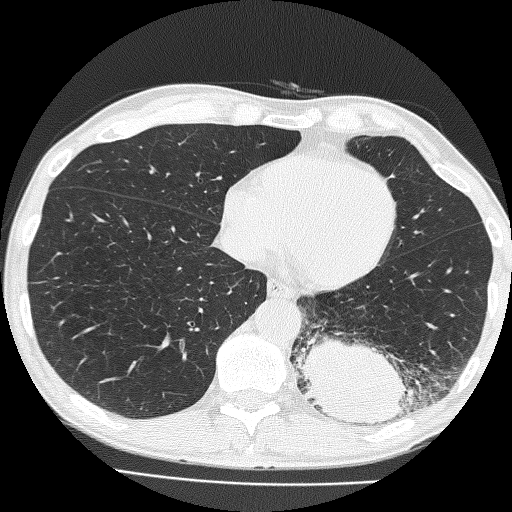
Low-dose screening chest CT, axial slice. Baseline annual screen. Lung window (W 1500 / L -600 HU). 120 kVp. Male, age 58 years at enrolment. Current smoker at enrolment.
- Expert-annotated lung lesion, bounding box <292,296,429,435> (left, top, right, bottom; pixels).
- The screening reader recorded 2 non-calcified nodules or masses ≥4 mm on this exam (left lower lobe, left upper lobe); which of them this box marks is not recorded.